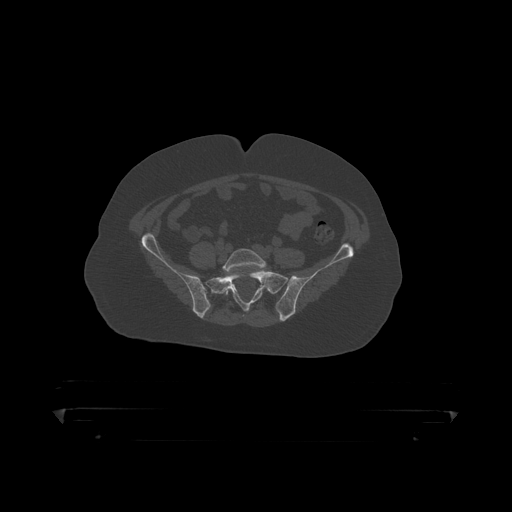
CT including the spine, one axial slice. Position 26 of 390 along the scan axis. Reconstruction kernel STANDARD. 120 kVp. Bone window (W 1800 / L 400 HU). 1.25 mm slice thickness. 512 × 512 image matrix, field of view 650 × 650 mm. Patient: male, 60 years. Case-level facts recorded for this patient, not image findings: primary cancer: prostate.
Outlined on this slice (semi-automatically segmented with operator editing):
- L5 vertebra: bounding box (x1, y1, x2, y2) in pixels: (224, 249, 267, 297)